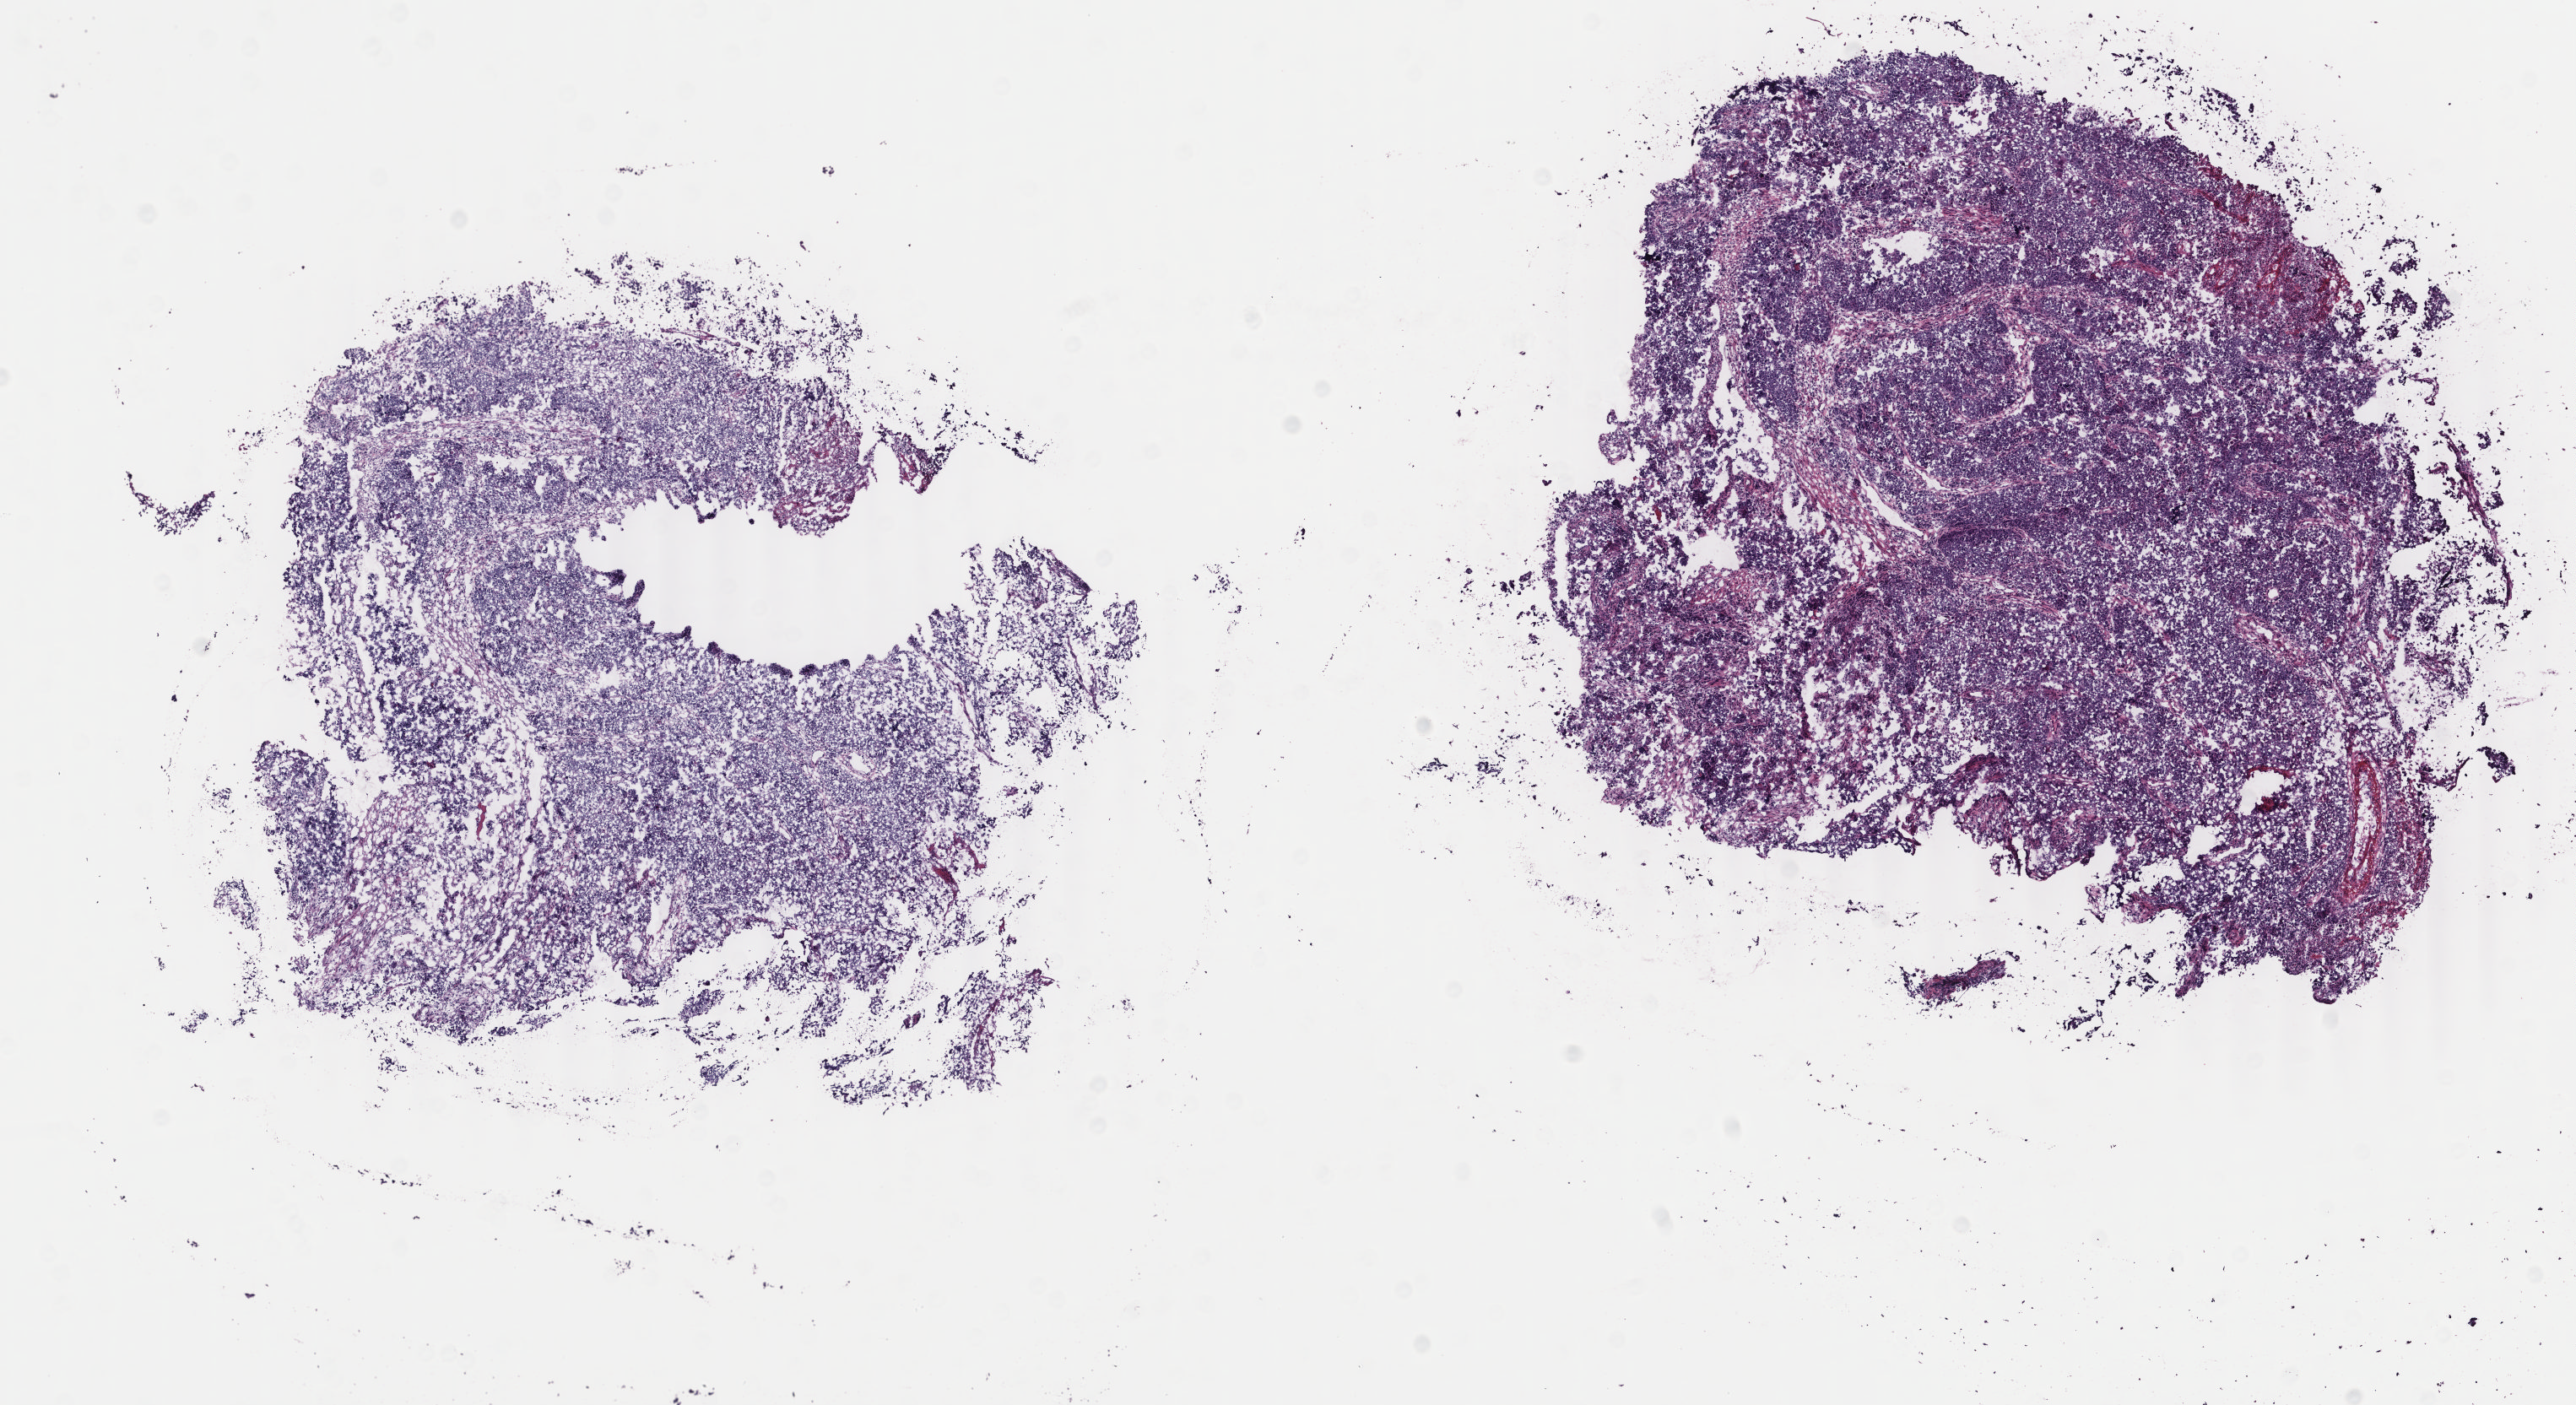
Whole-slide histology image, H&E-stained — shown as a low-resolution overview of the whole scanned area (about 12.1 x 6.6 mm). Frozen section from the bottom of the tissue portion. Uterus, primary tumour sample. Female, age 55 years at initial diagnosis. Histologic grade: G3 (poorly differentiated). Composition of this section per pathologist review: tumour cells 75%, tumour nuclei 90%, normal cells 0%, stromal cells 10%, necrosis 15%. Inflammatory infiltration, as recorded: lymphocyte infiltration 40%, monocyte infiltration 0%, neutrophil infiltration 57%.
FIGO stage: IIIC. Pathologic diagnosis: Endometrioid adenocarcinoma, NOS (endometrium). Lymph nodes positive (case pathology): 1 of 8 examined.